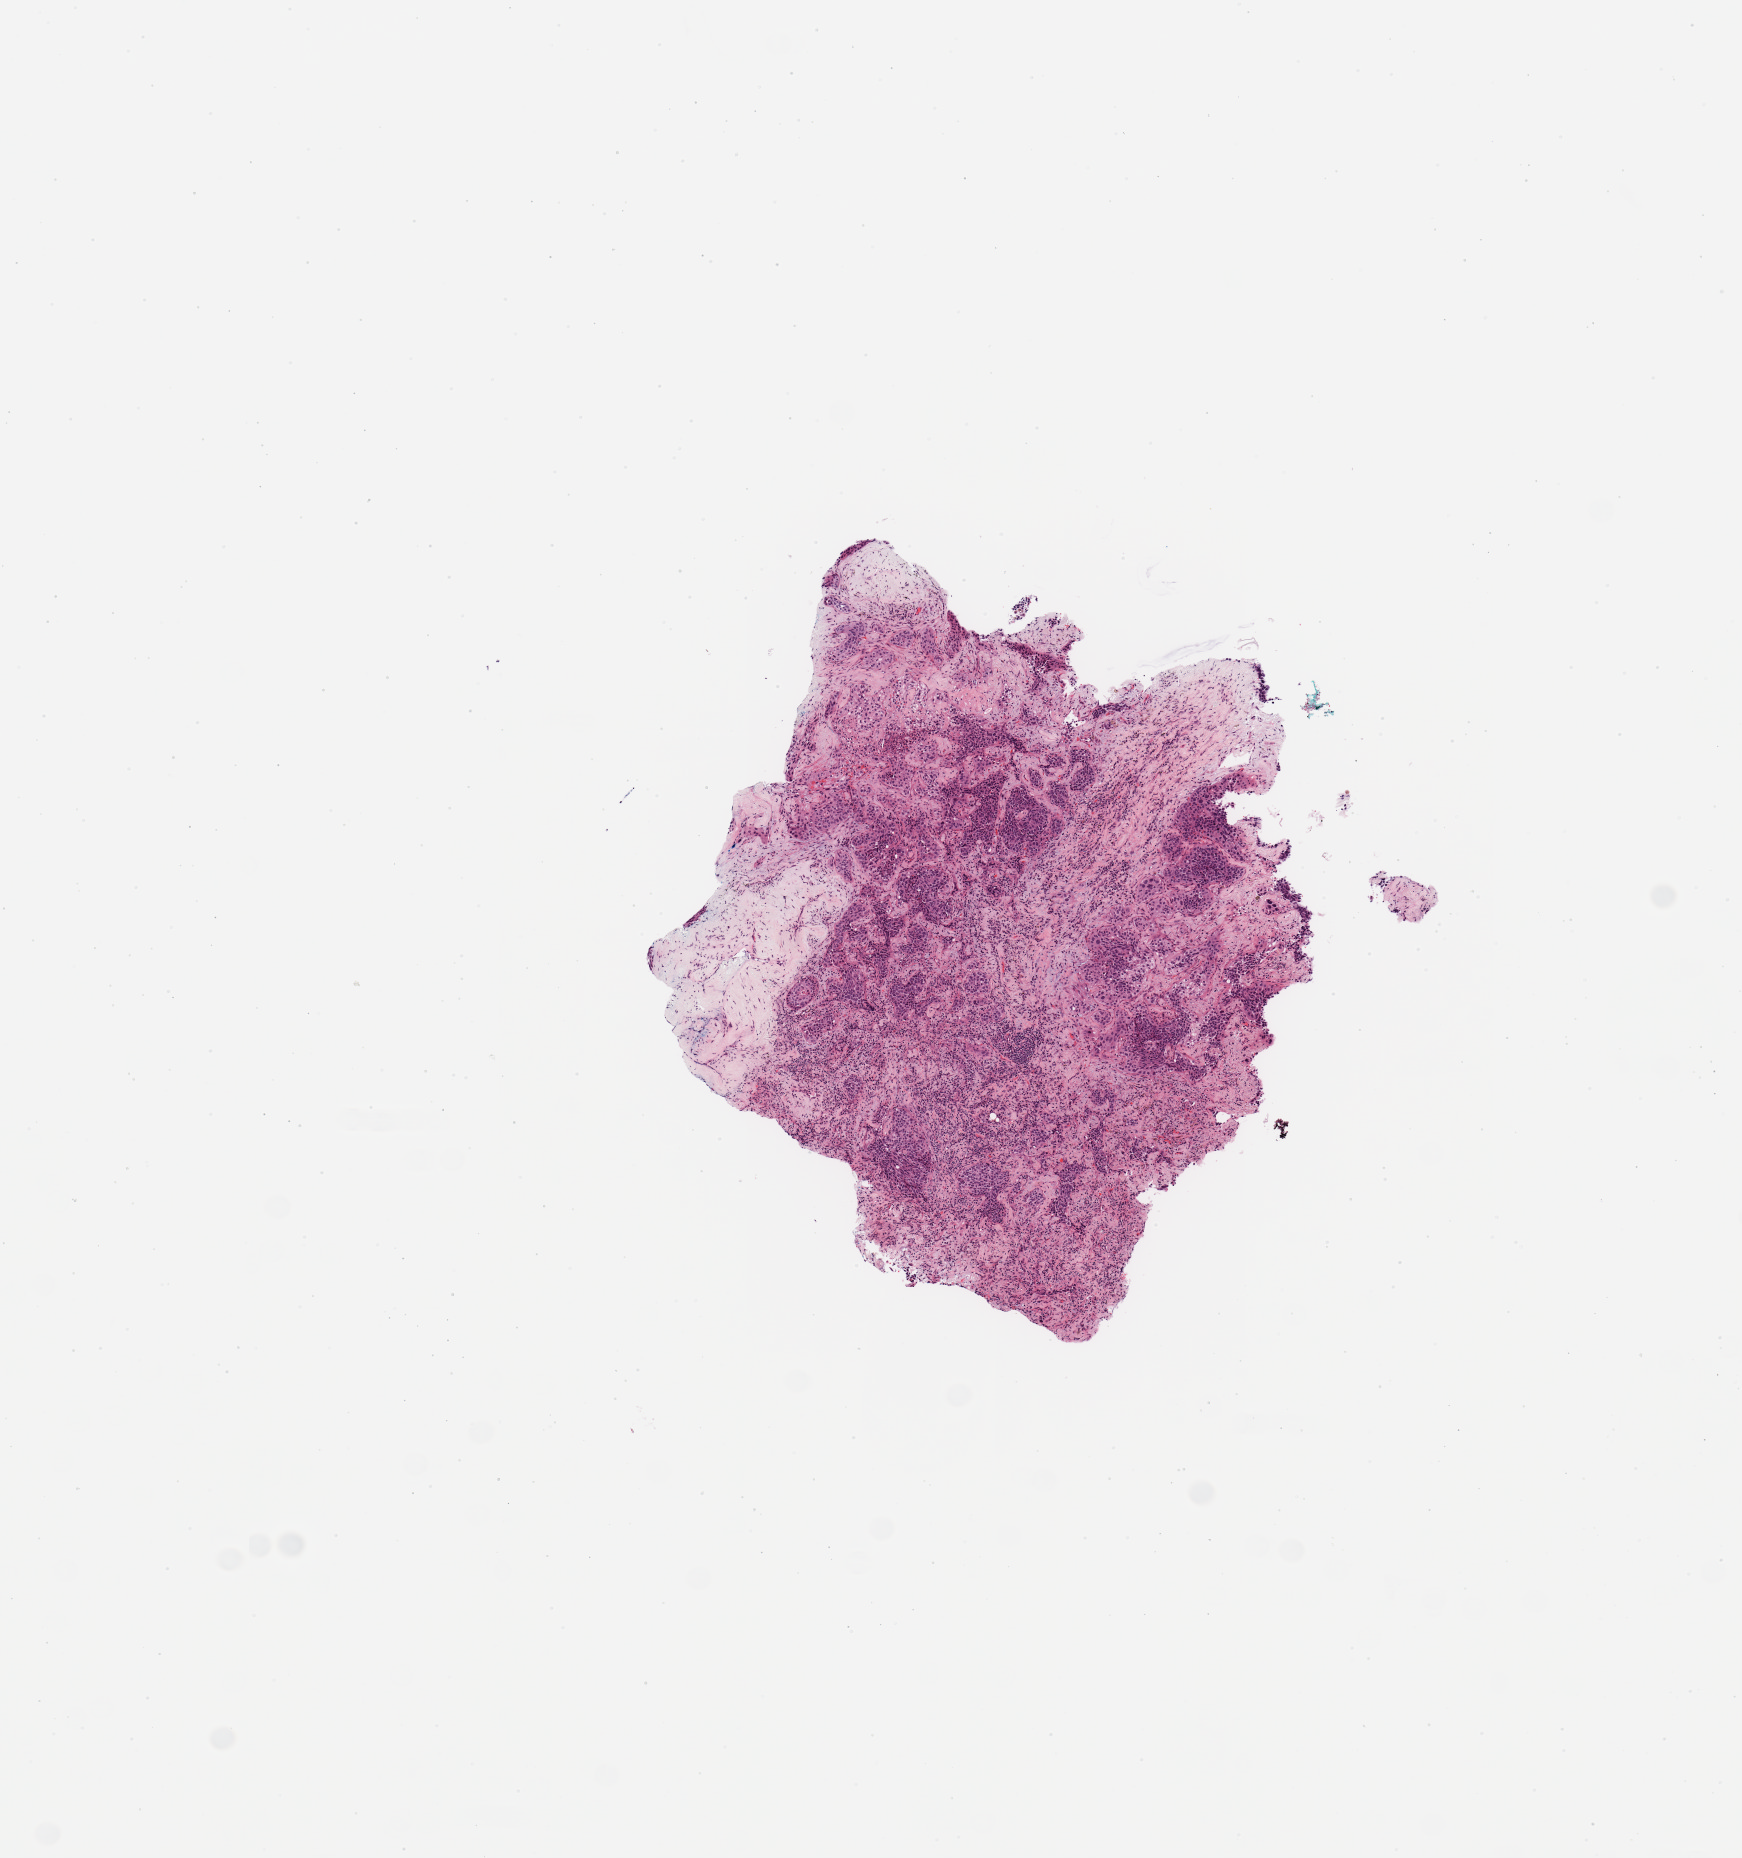
Whole-slide histology image, H&E-stained — whole scanned area (about 6.9 x 7.3 mm, slide scanned at 20x) shown as a low-resolution overview. Tumour tissue sample, lung. Female, 73 y/o. Histologic grade: G3 (poorly differentiated).
• primary tumour site (as recorded): right upper lobe
• AJCC pathologic stage: IIIA
• diagnosis: Squamous cell carcinoma, NOS